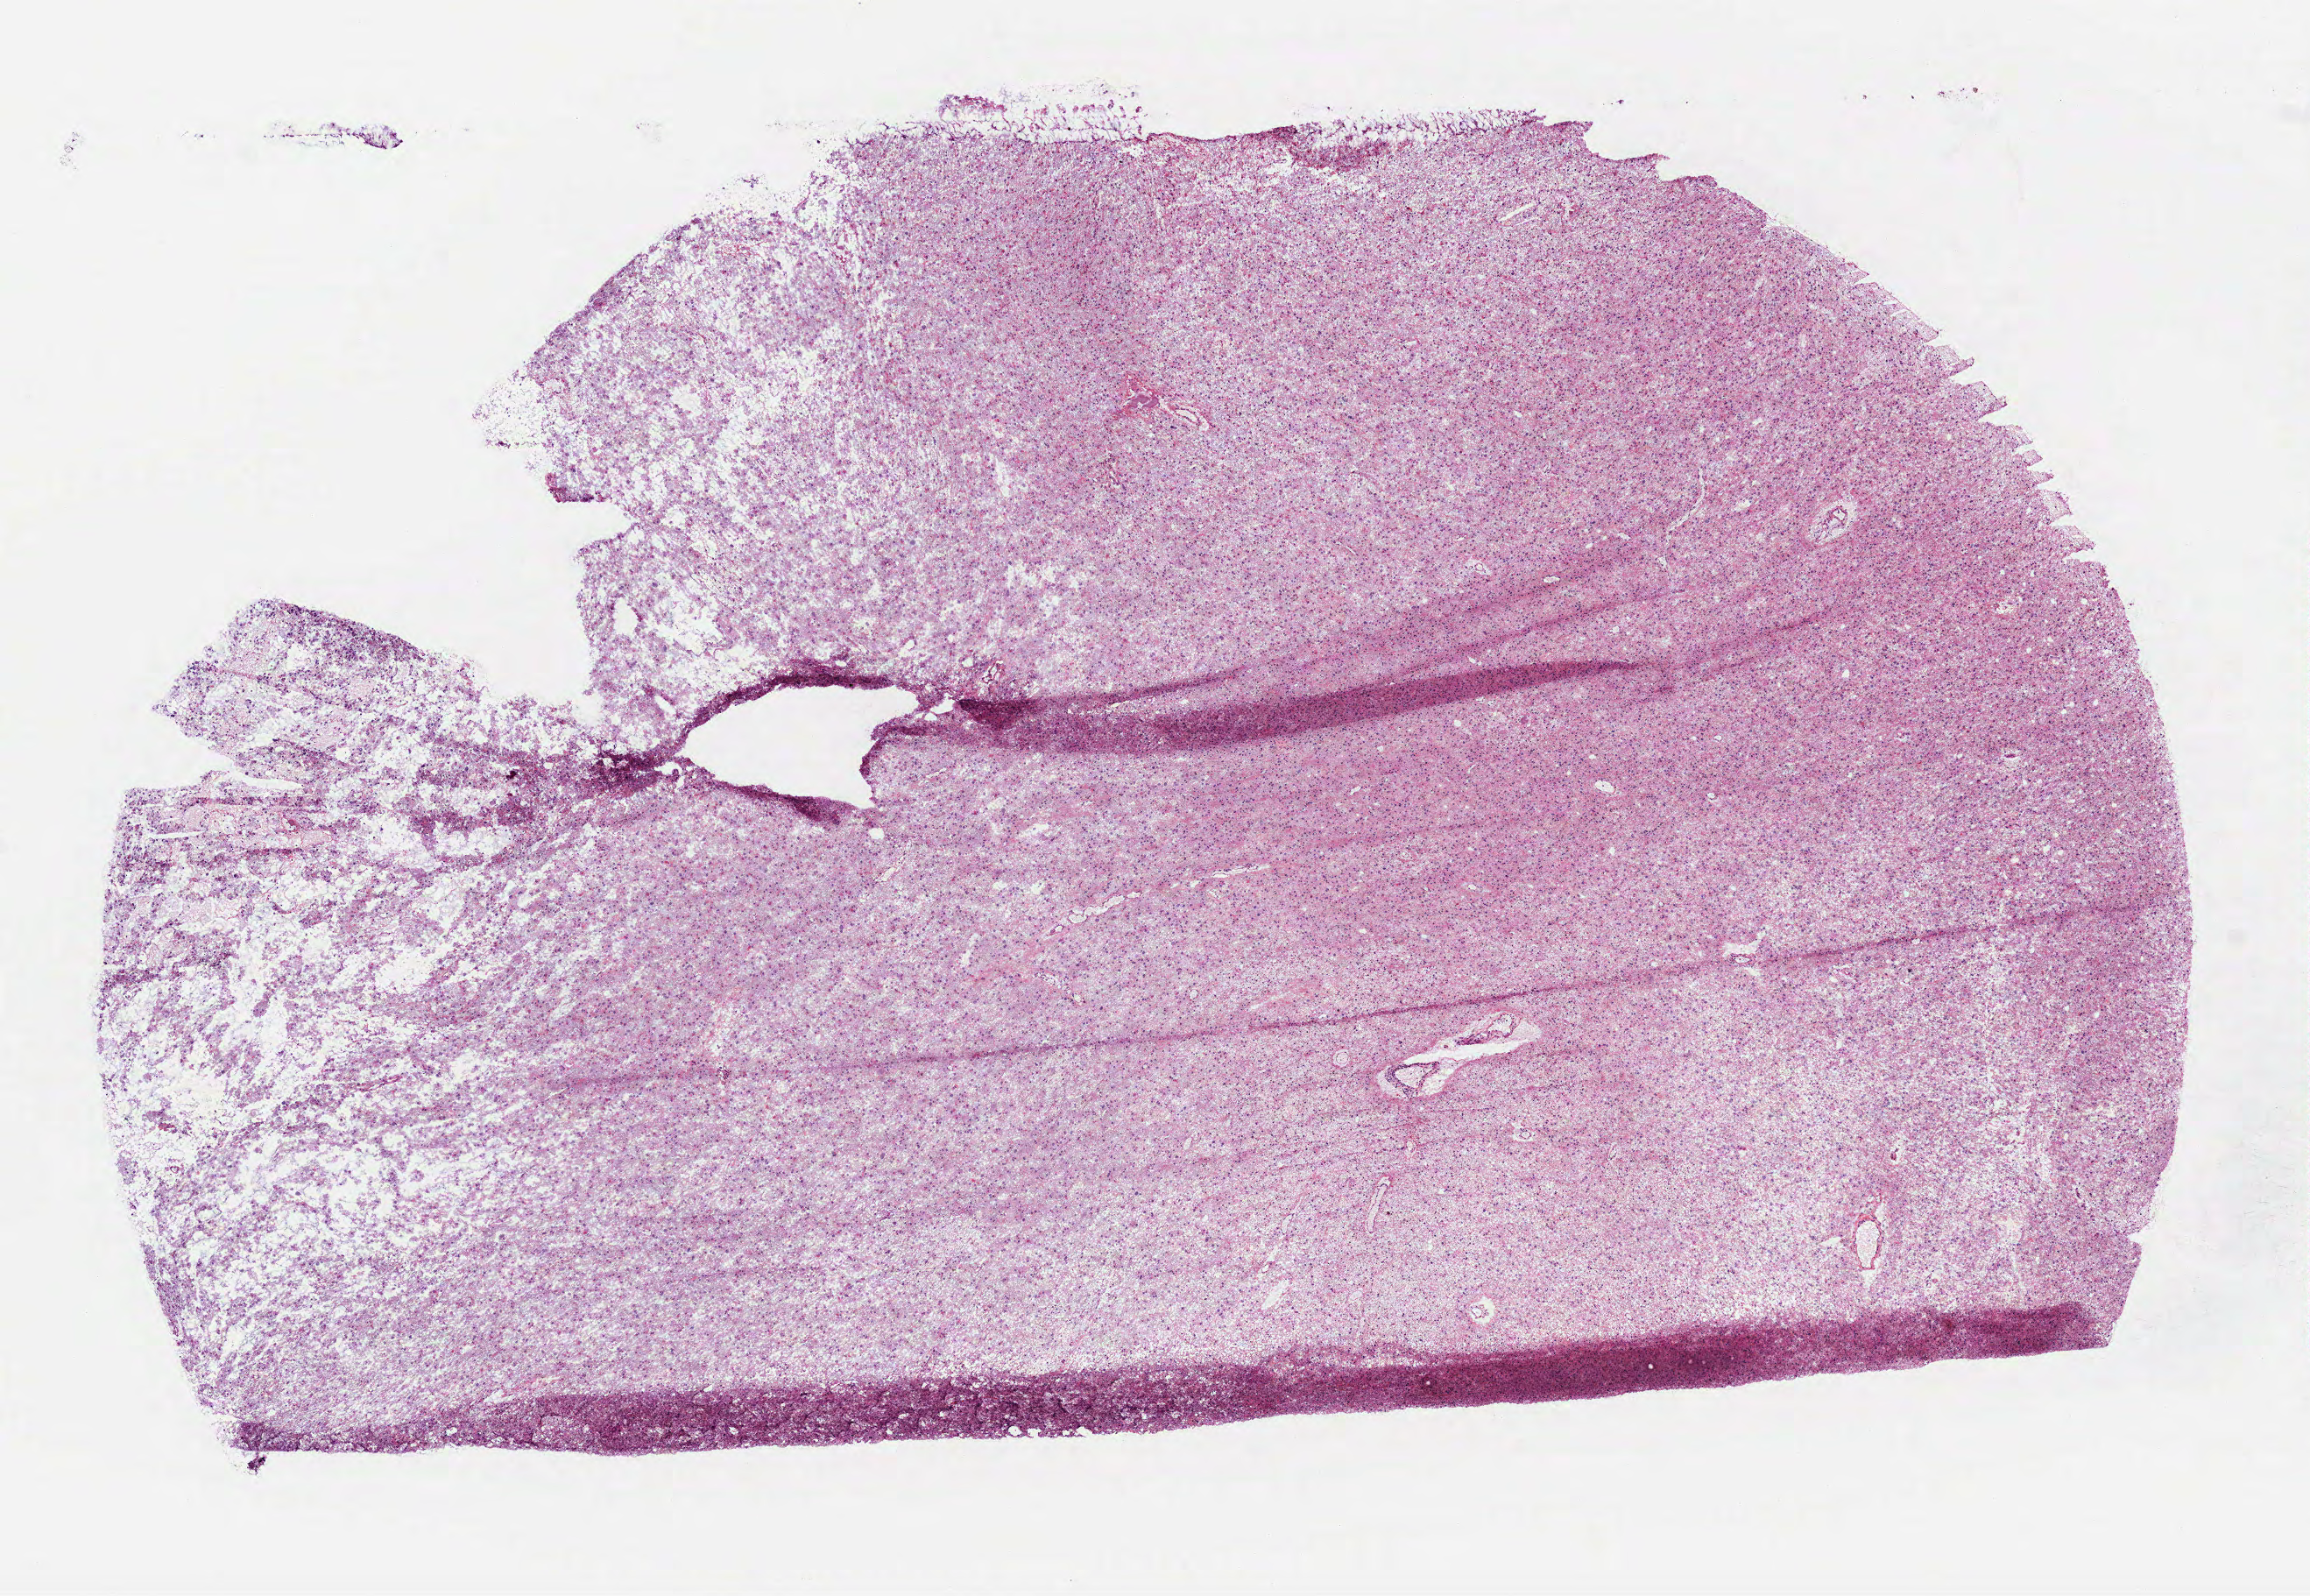
Digitized H&E tissue section (whole slide), shown as a low-resolution overview of the whole scanned area (about 10.6 x 7.3 mm, acquisition: 40x scan). Frozen section from the bottom of the tissue portion. Sample: primary tumour, brain. Male patient; age at initial diagnosis 43 years. Histologic grade: G3 (poorly differentiated). Slide review estimates, as recorded: tumour cells 100%, tumour nuclei 75%, normal cells 0%, stromal cells 0%, necrosis 0%.
* pathologic diagnosis: Mixed glioma (cerebrum)